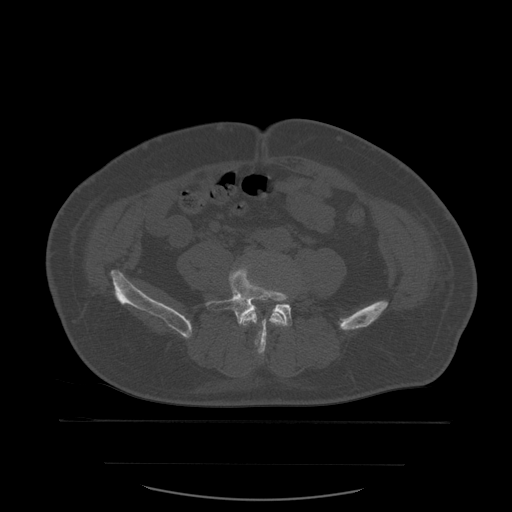
CT including the spine, one axial slice; position 148 of 590 along the scan axis; bone window (W 1800 / L 400 HU); 1.25 mm slice thickness; 512 × 512 image matrix, field of view 479 × 479 mm. Patient age 71 years. Case-level facts recorded for this patient, not image findings: primary cancer: lung; vertebrae with lytic lesions (as recorded): T1, T2, L5, S1.
Annotated regions visible in this slice (semi-automatically segmented with operator editing):
- L4 vertebra: box from (x=242, y=310) to (x=286, y=347) px
- L5 vertebra: (x=206, y=265)–(x=293, y=354)